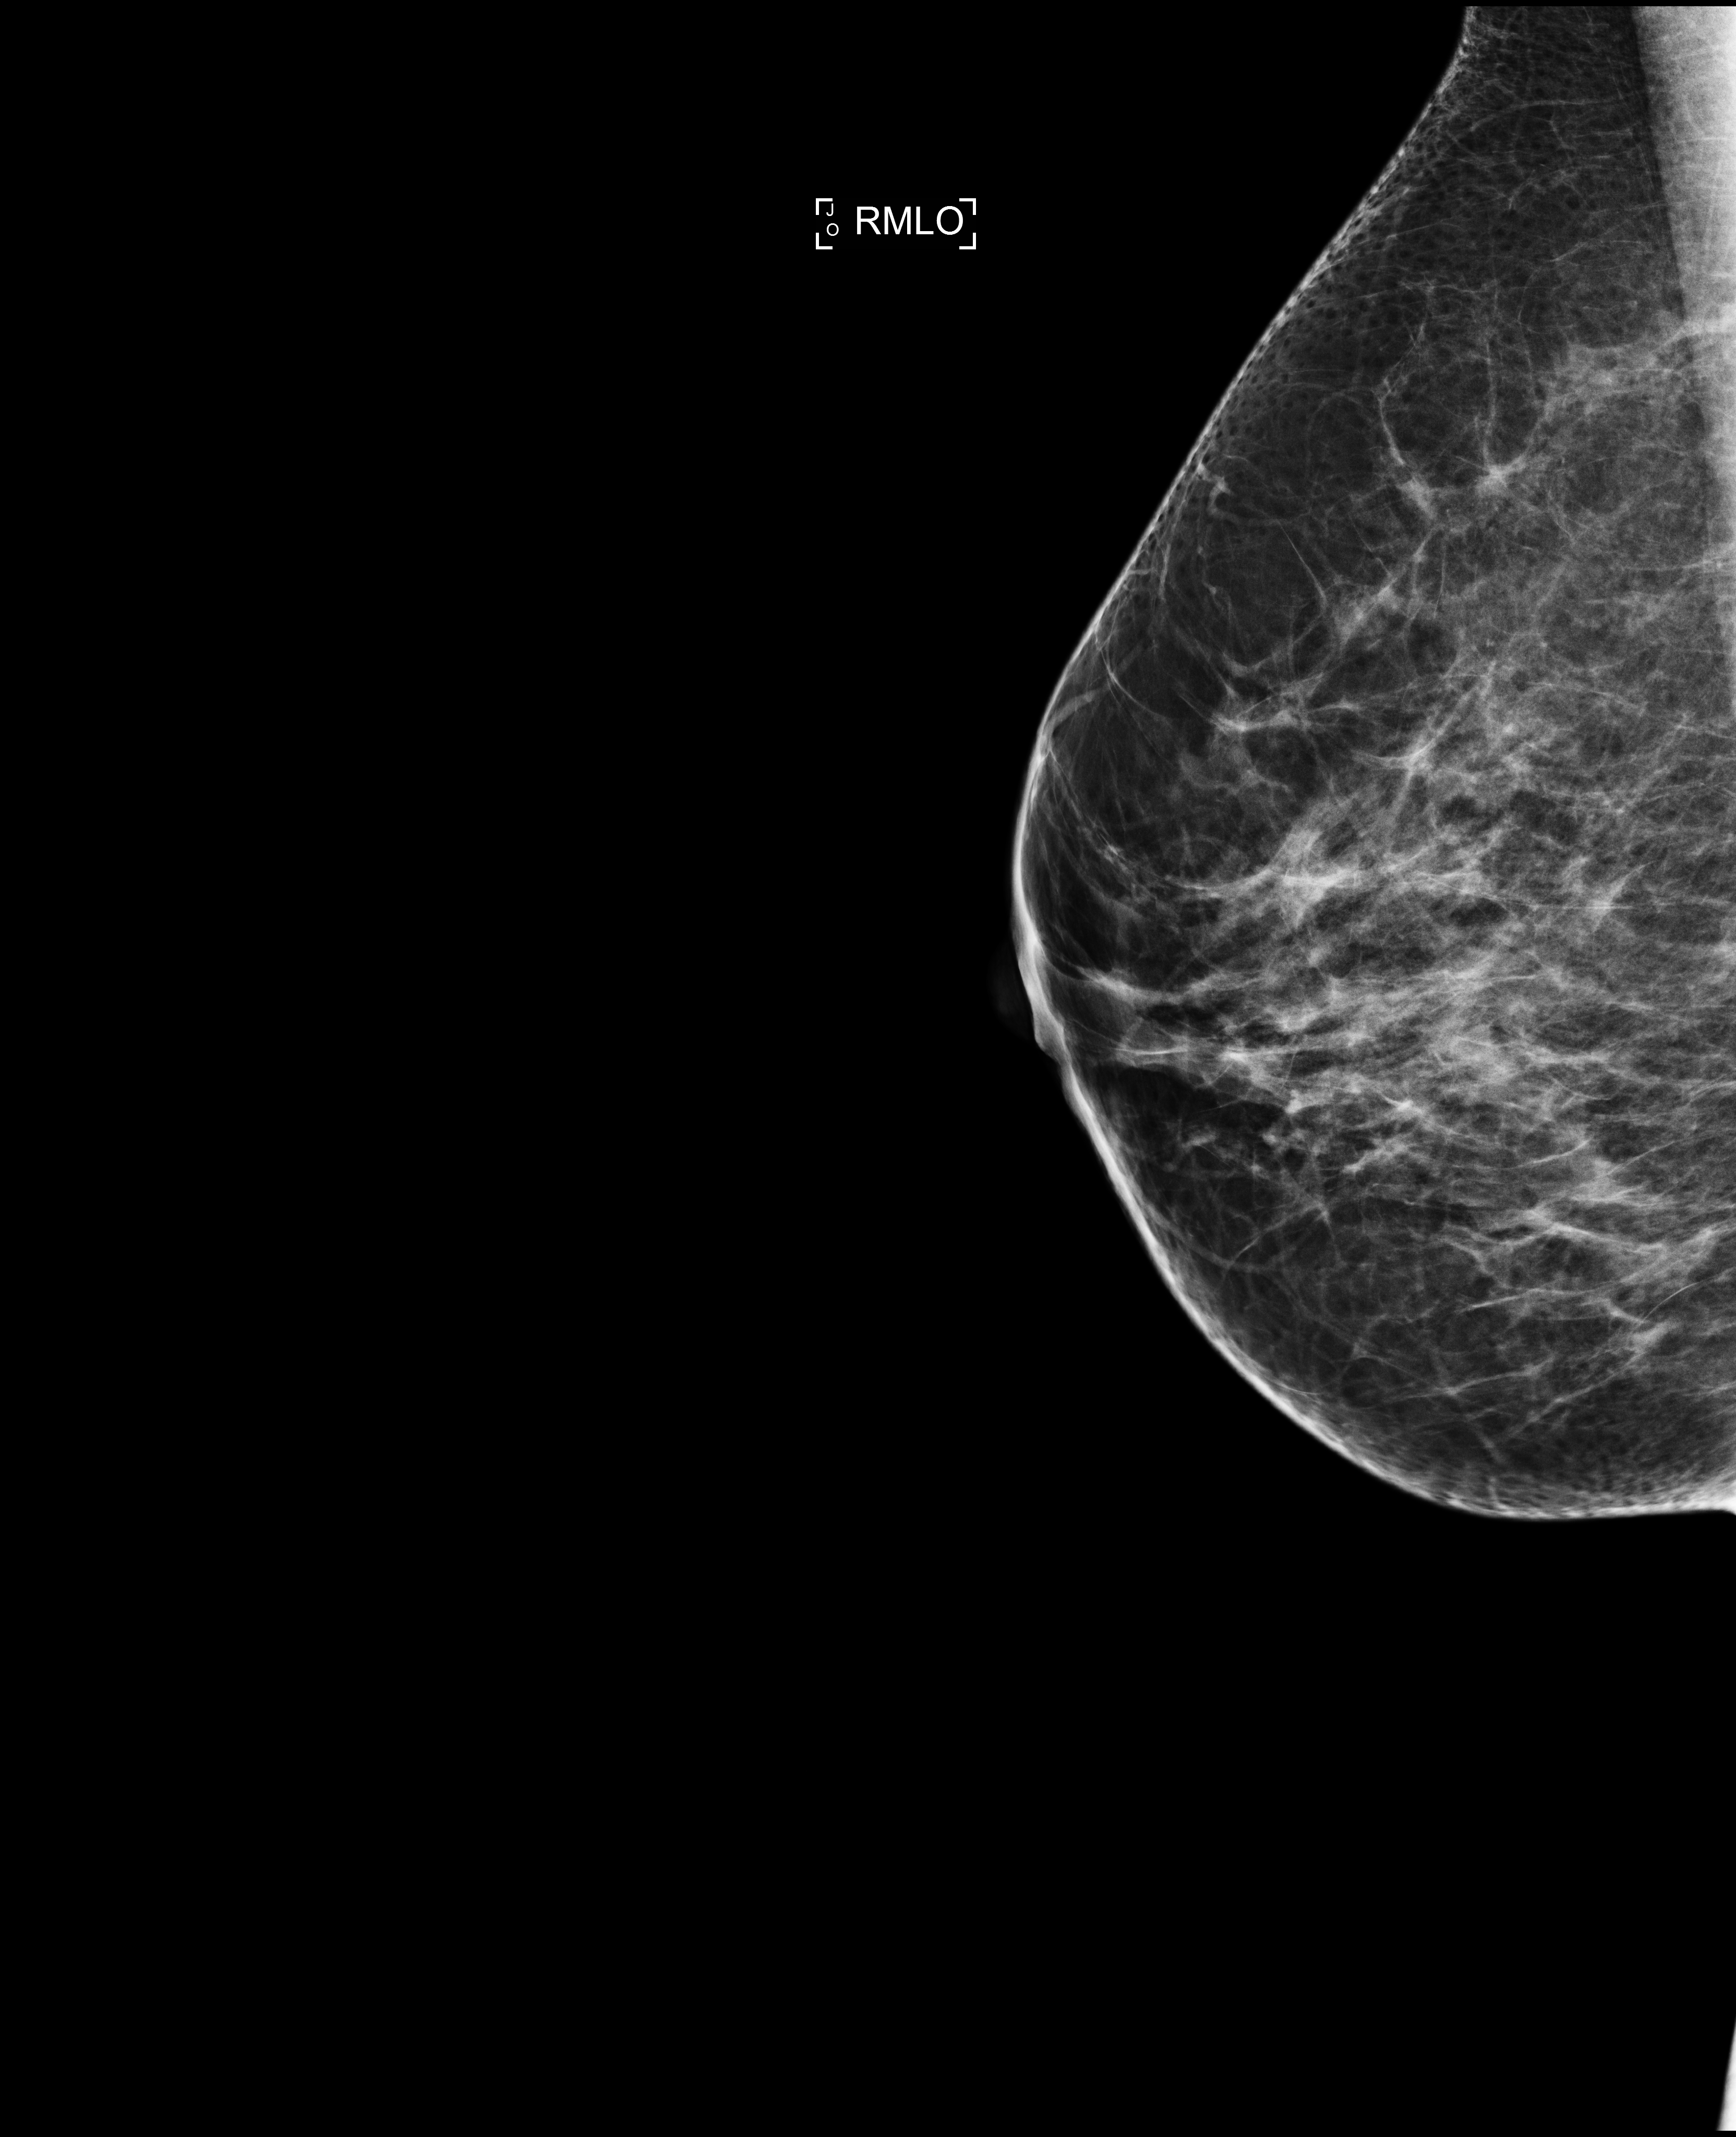
Screening examination; compressed breast thickness 66 mm. Patient aged 48 years (female).
Image type: full-field digital mammogram. Breast: right. Projection: medio-lateral oblique projection.